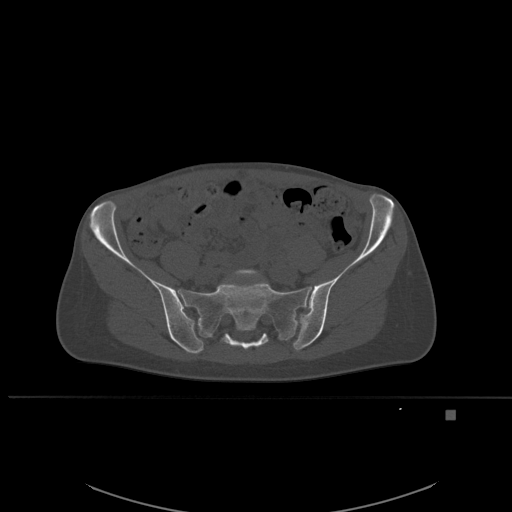
CT including the spine, one axial slice. Slice 154 of 537 in the series (ordered by position). Bone window (W 1800 / L 400 HU). 1.5 mm slice thickness. 512 × 512 image matrix, field of view 440 × 440 mm. Patient: female, 45 years. Case-level facts recorded for this patient, not image findings: primary cancer: lung.
Annotated regions visible in this slice (semi-automatic segmentation, software-assisted and operator-edited):
- L5 vertebra: bounding box [x1, y1, x2, y2] px = [232, 269, 260, 278]